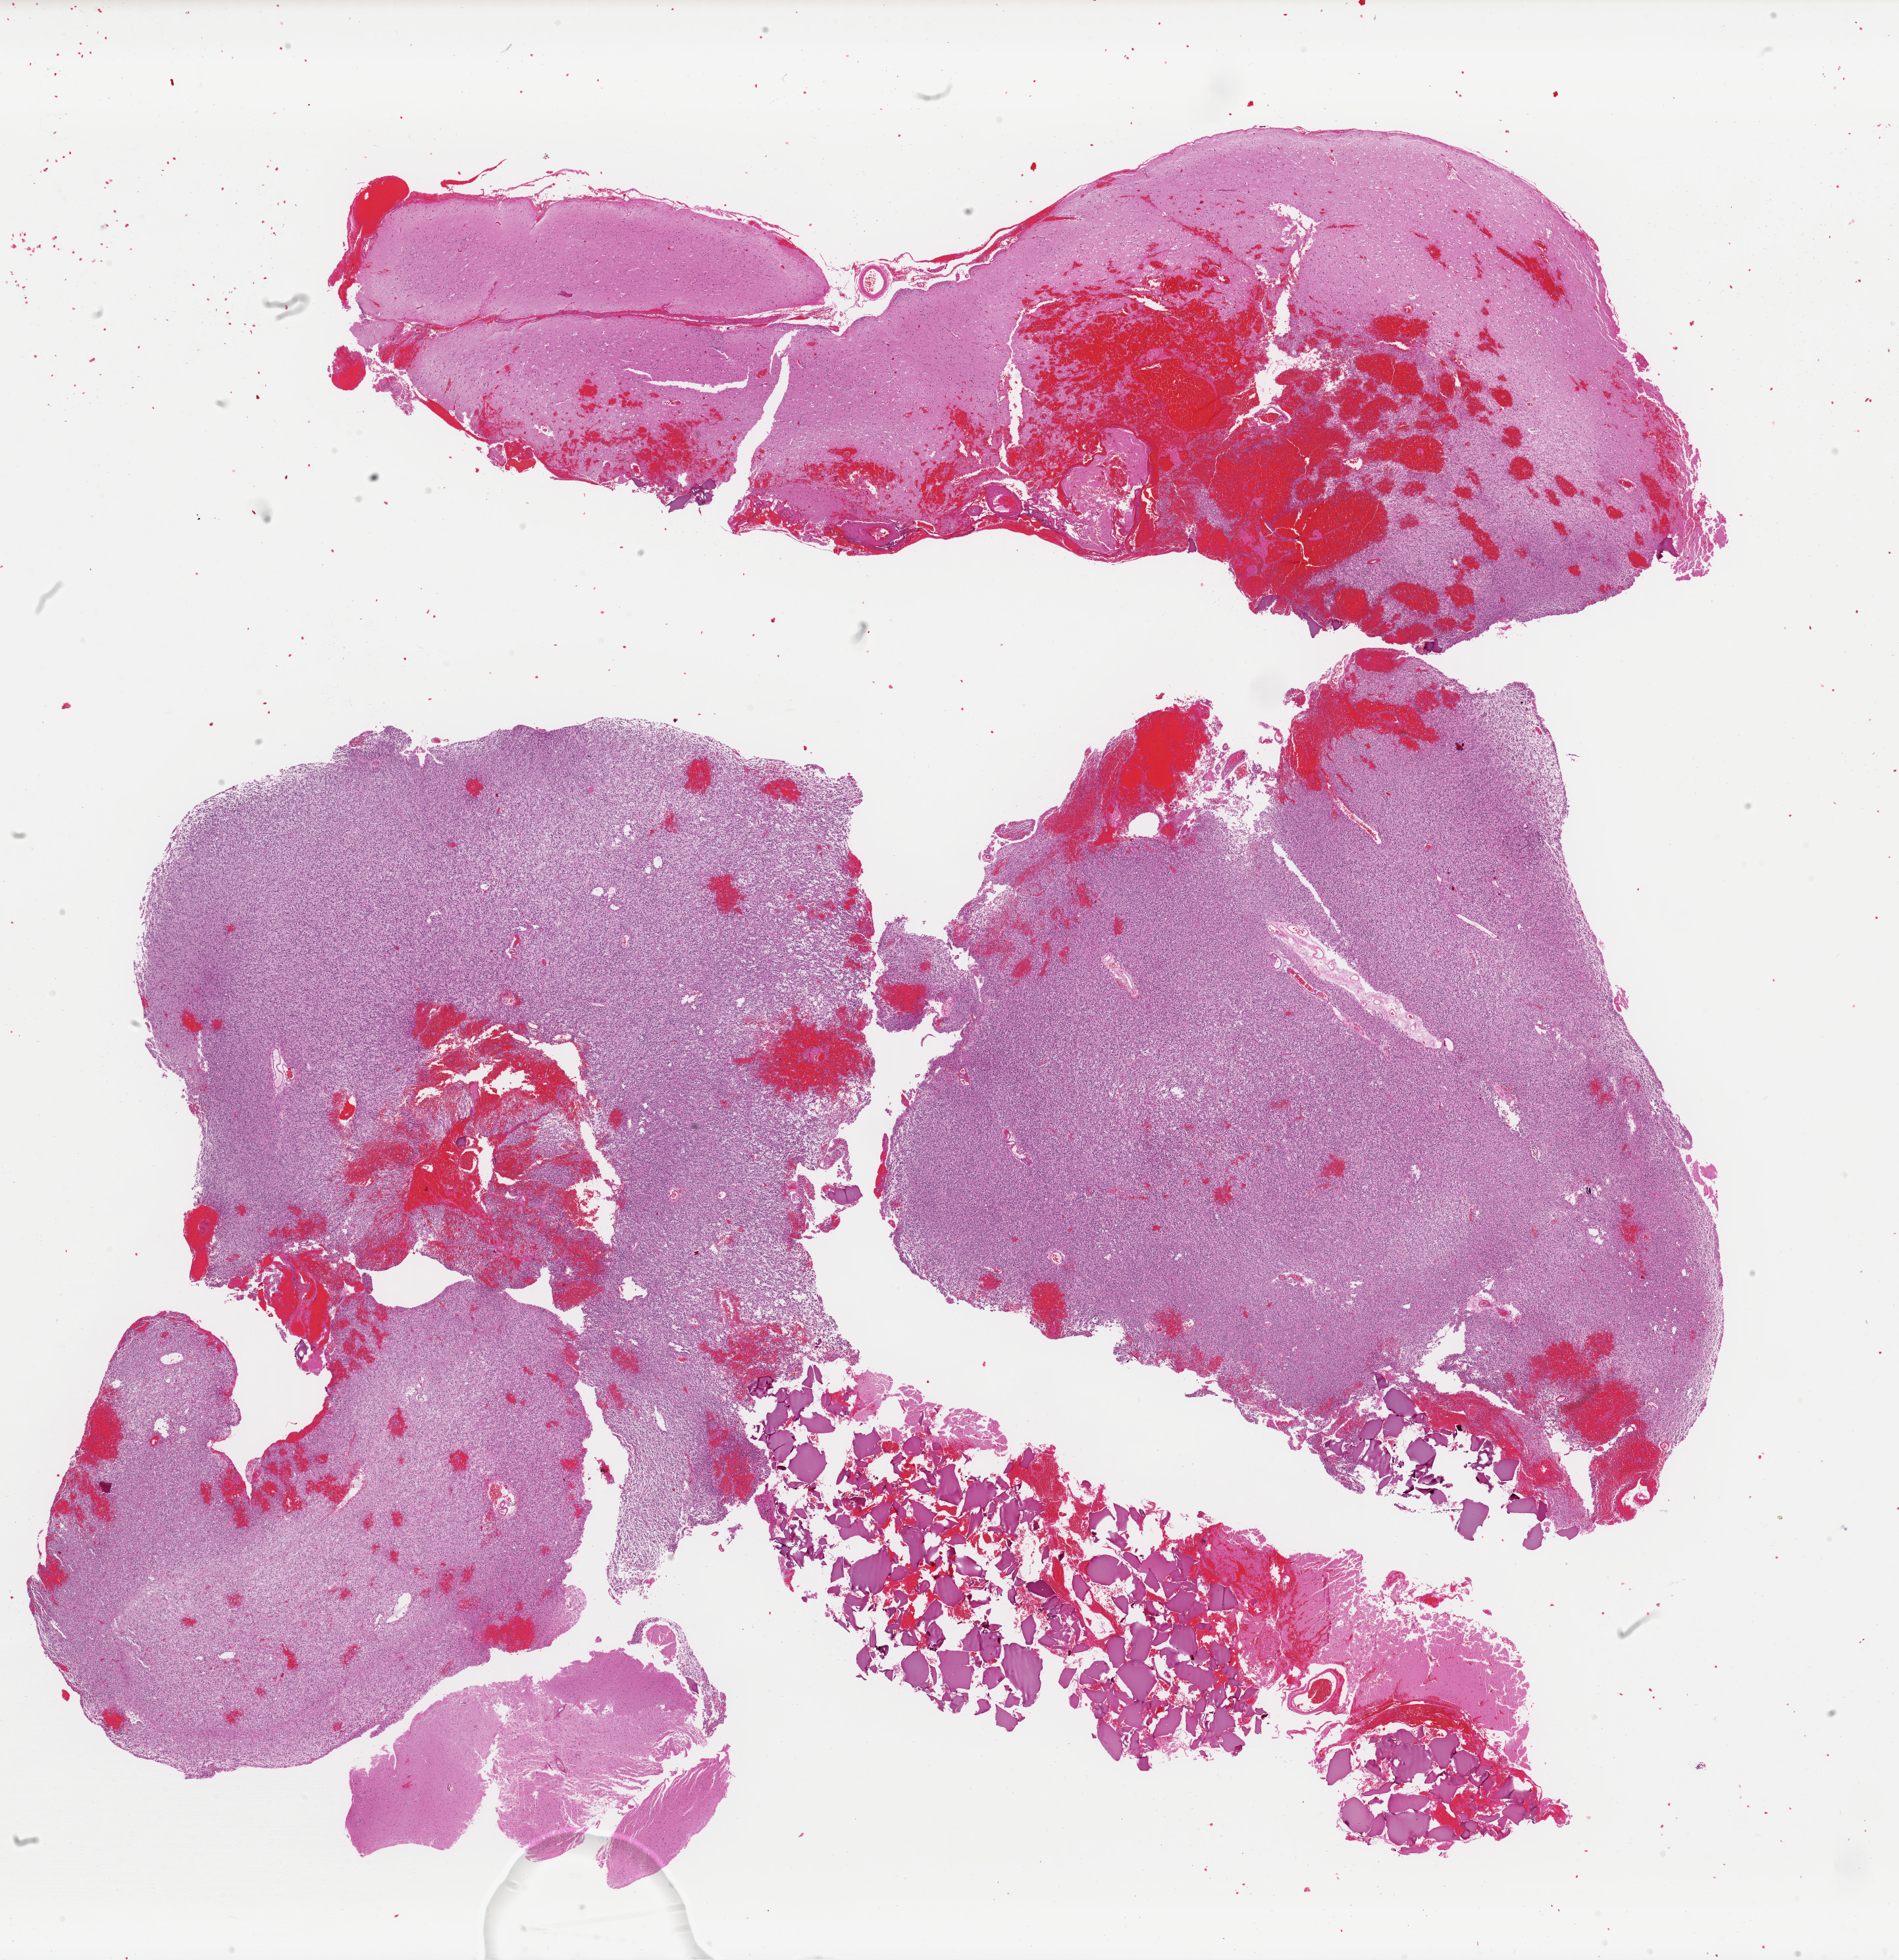
Digitized H&E-stained tissue section (whole slide) — shown as a low-resolution overview of the whole scanned area (about 22.8 x 23.5 mm, slide scanned at 40x). Formalin-fixed paraffin-embedded (FFPE) diagnostic section. Sample: recurrent tumour, brain. Female patient; age at initial diagnosis 27 years.
This section: recurrent tumour. Patient diagnosis: Oligodendroglioma, NOS (temporal lobe).